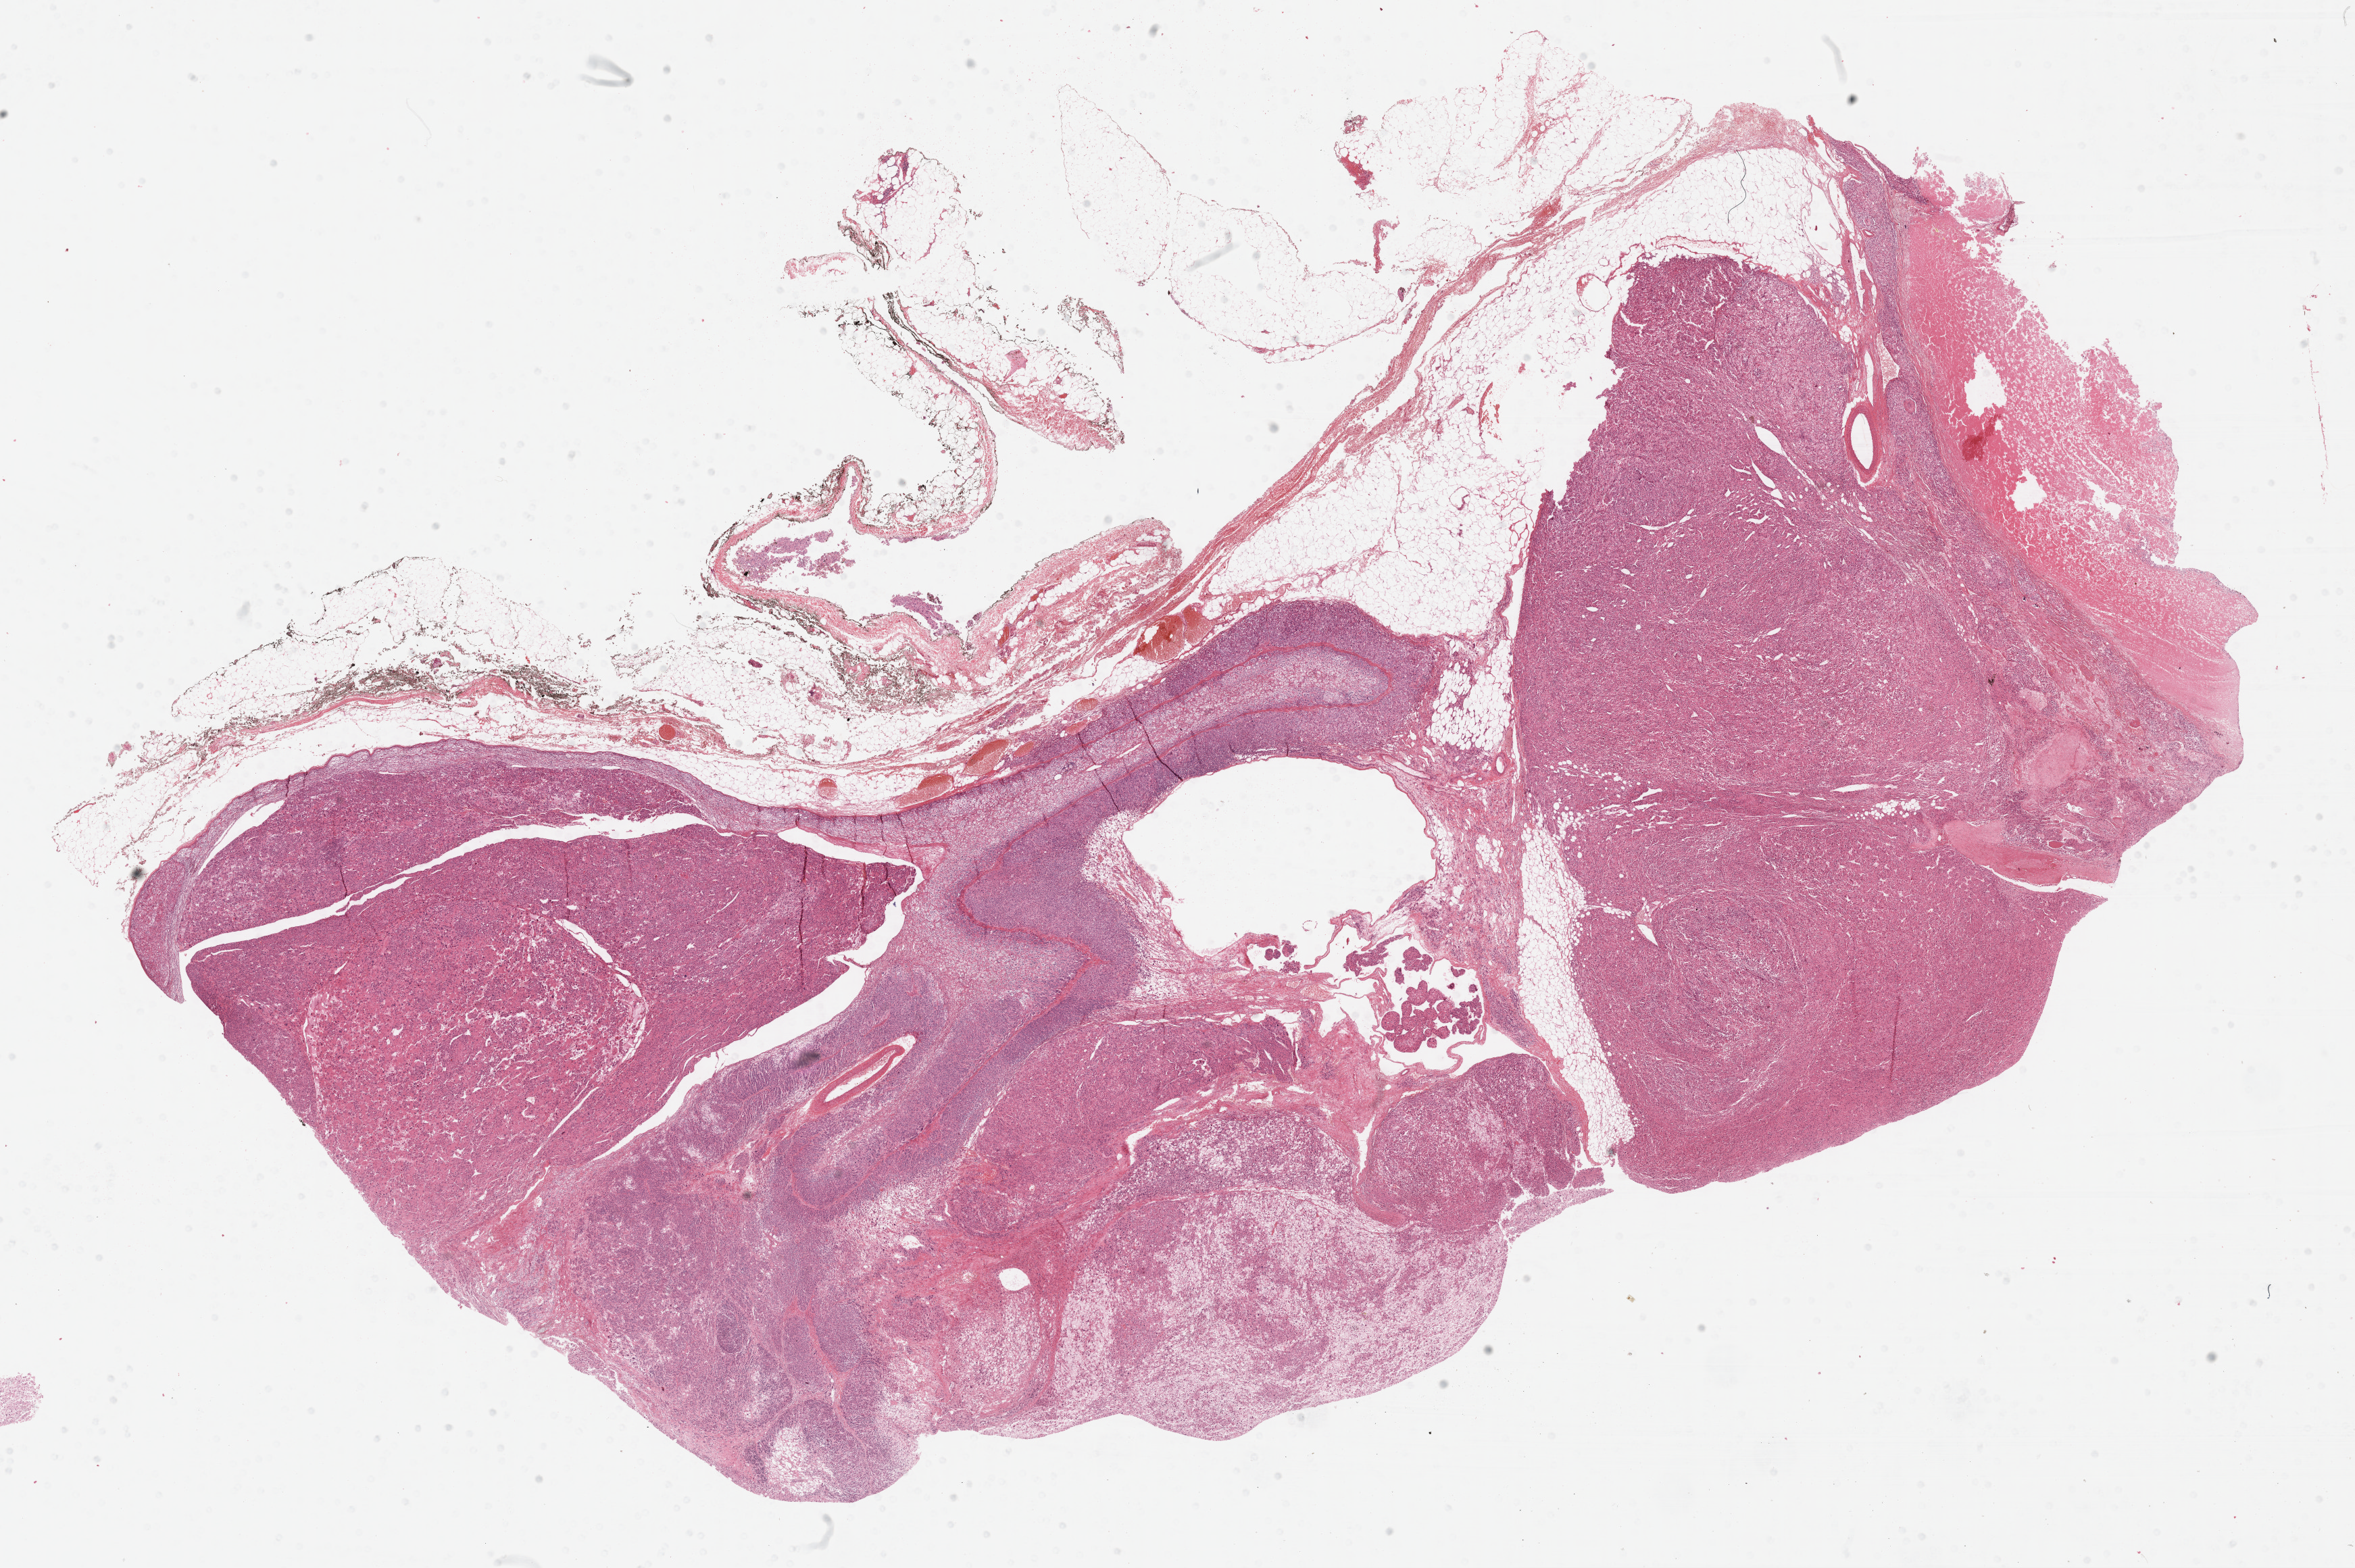
H&E whole-slide image — a low-resolution overview of the entire scanned area, about 28.2 x 18.8 mm (from a 40x scan). Formalin-fixed paraffin-embedded (FFPE) diagnostic section. Primary tumour sample from the adrenal cortex. Patient: female, age at initial diagnosis 30 years.
* histologic diagnosis: Adrenal cortical carcinoma (cortex of adrenal gland)
* laterality: right